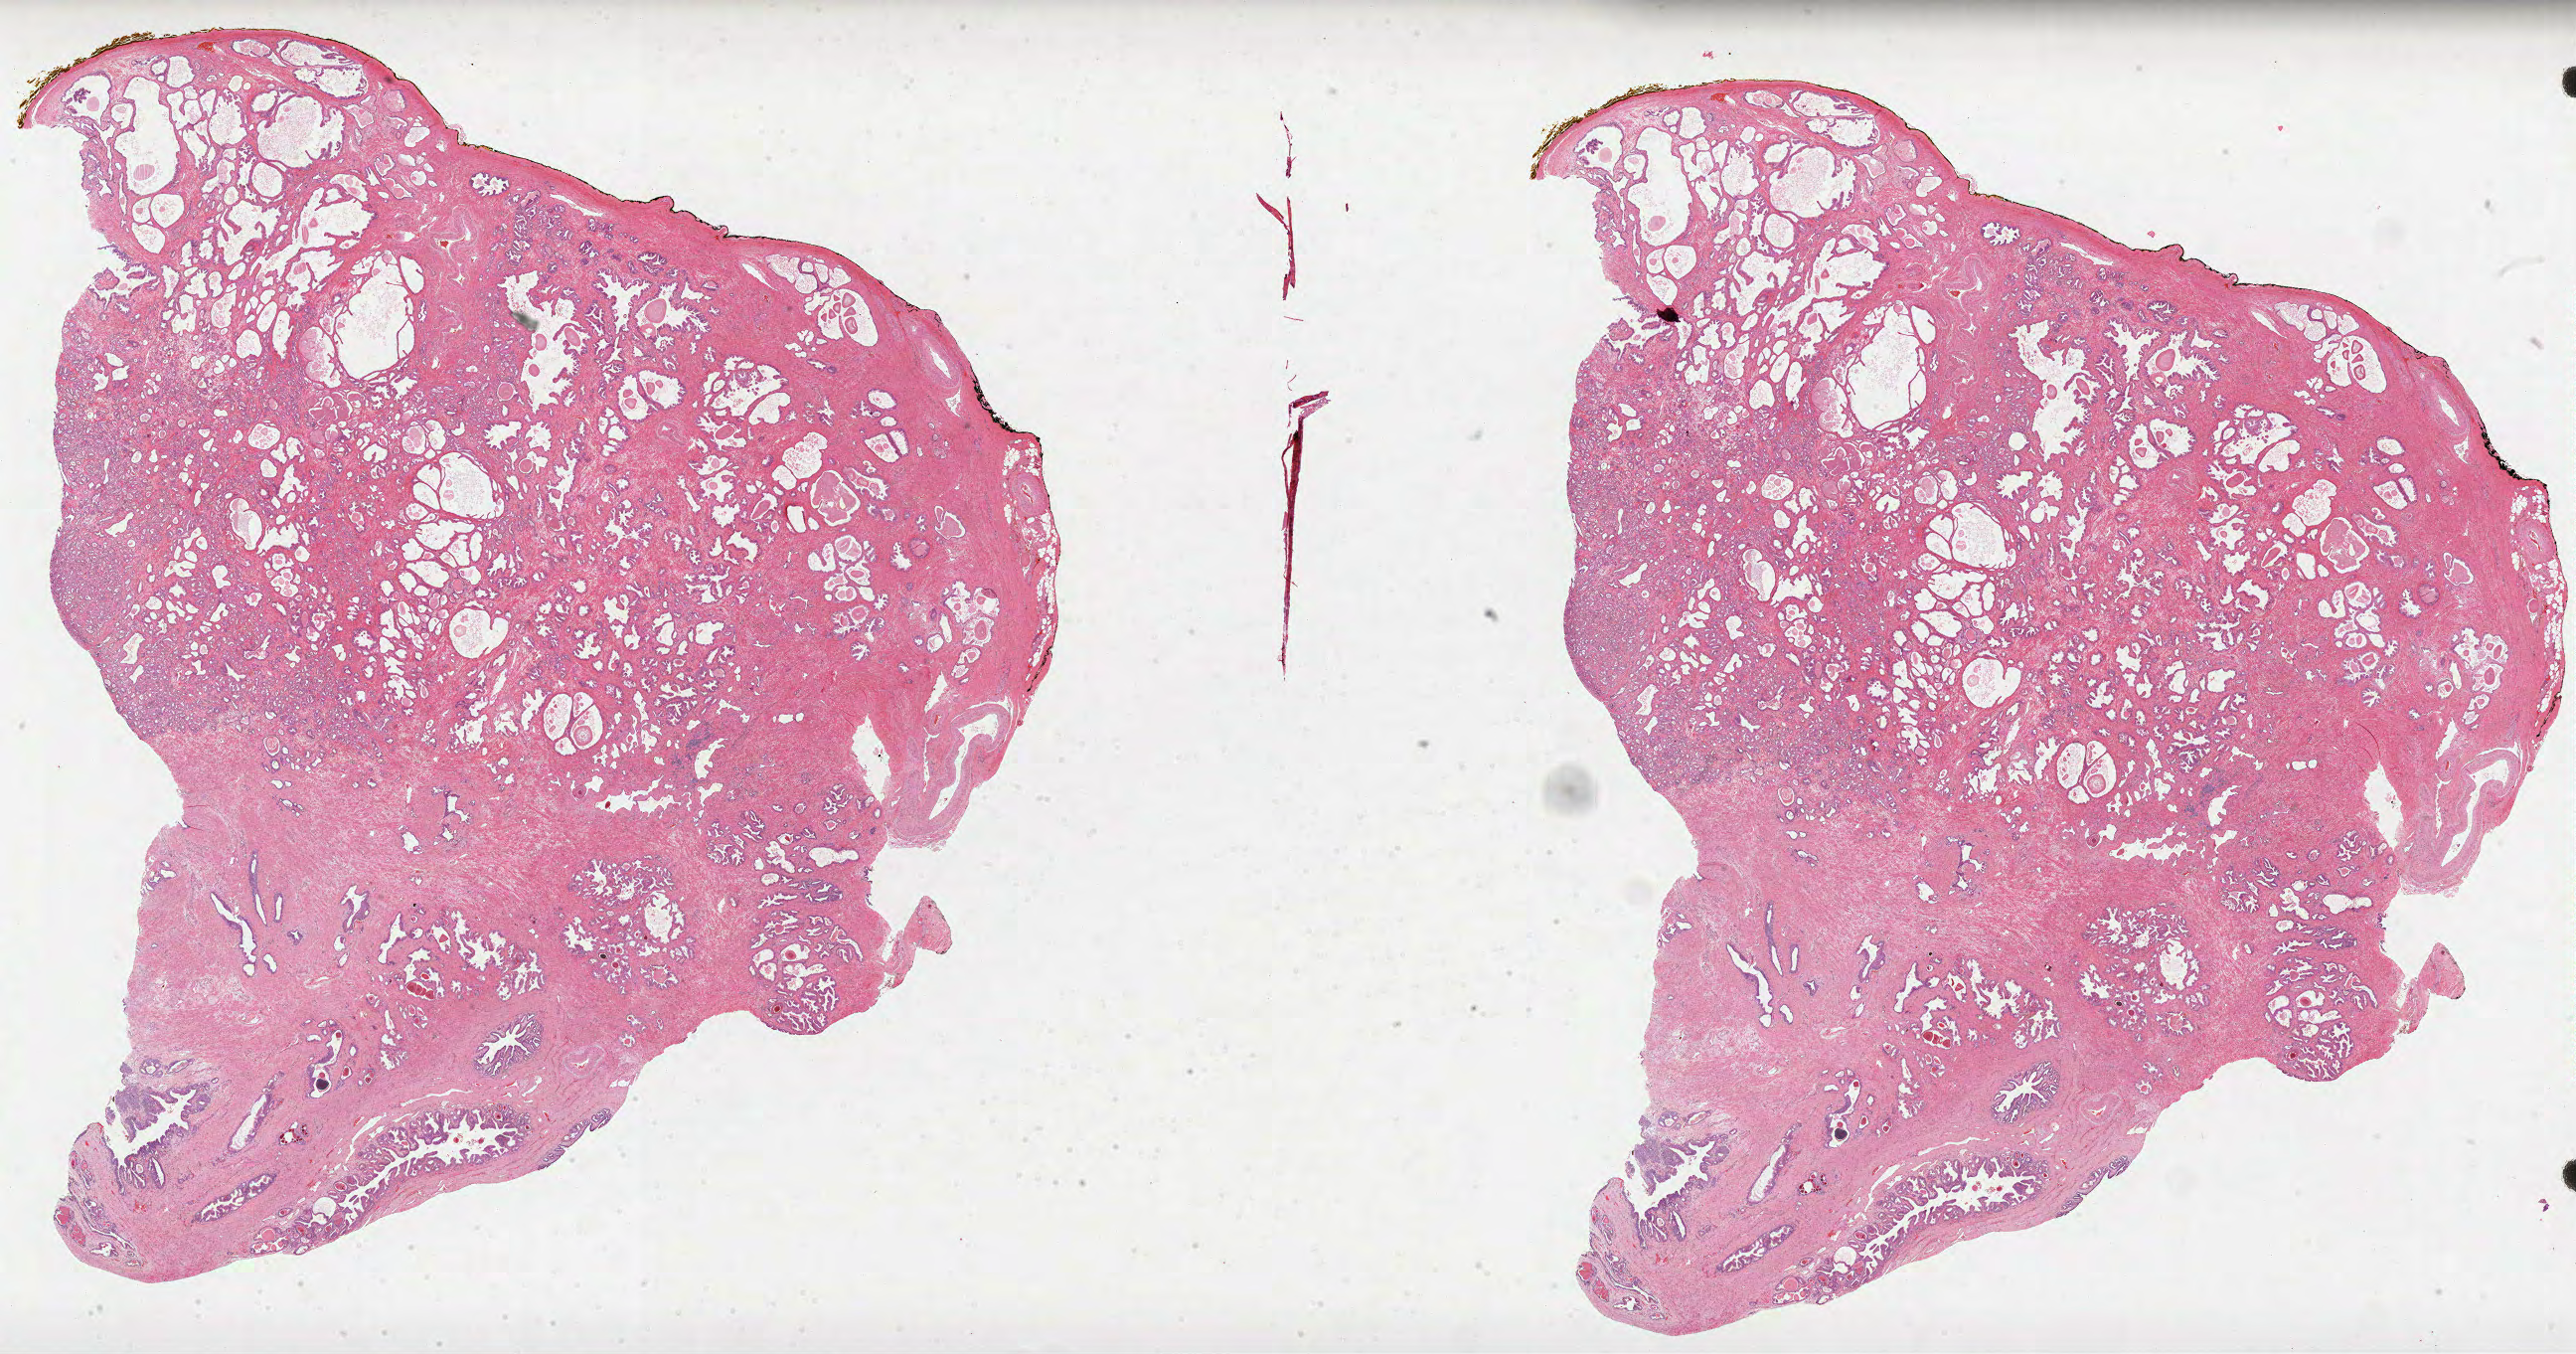
Digitized H&E tissue section (whole slide) — a low-resolution overview of the entire scanned area, about 41.8 x 22.0 mm (slide scanned at 40x), FFPE section, prostate, primary tumour sample. Male, age 58 years at initial diagnosis. Gleason score: 6 (3+3).
- pathologic diagnosis: Acinar cell carcinoma (prostate gland)
- laterality: bilateral